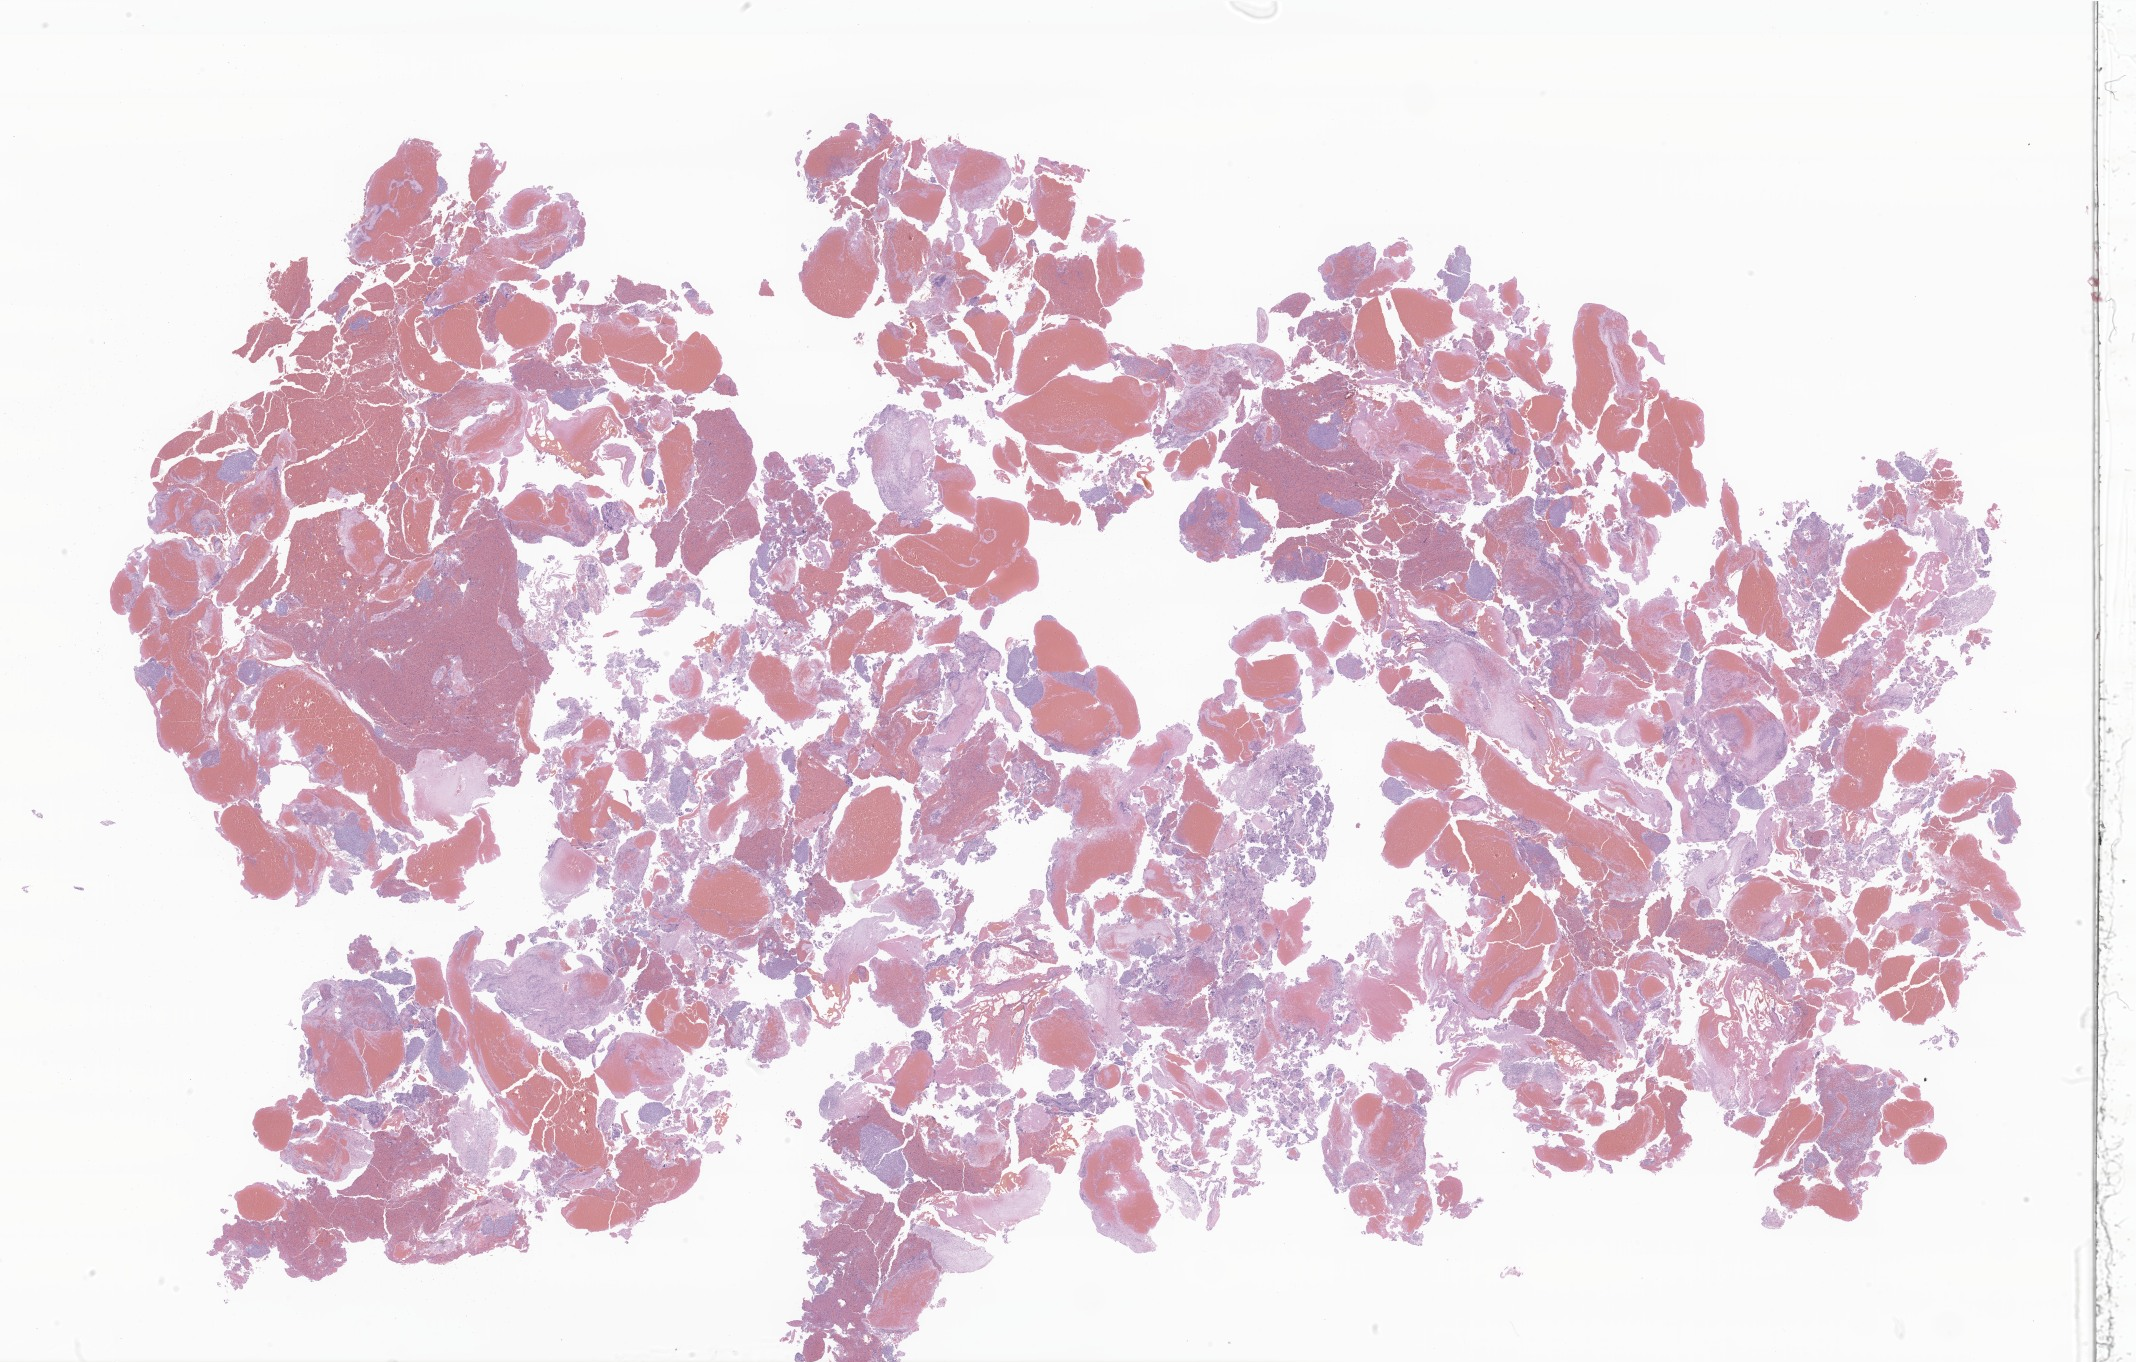
Haematoxylin and eosin whole-slide image of tumor tissue from the pineal gland, shown as a low-resolution overview of the whole scanned area (about 36.0 x 23.0 mm), formalin-fixed paraffin-embedded section. Patient: male, age 34 months (2 years 10 months).
- diagnosis: Atypical teratoid/rhabdoid tumor